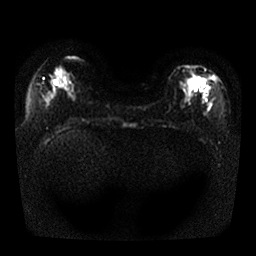
Breast MRI, one axial slice; diffusion-weighted series; image 2 of 4 stored at this slice position (different b-values; order by instance number); 1.5 T; 4 mm slice thickness; 256 × 256 image matrix. Female patient.
Annotated regions visible in this slice (expert manual segmentation):
- tumour on diffusion-weighted imaging: bounding box (x1, y1, x2, y2) in pixels: (185, 75, 201, 91)